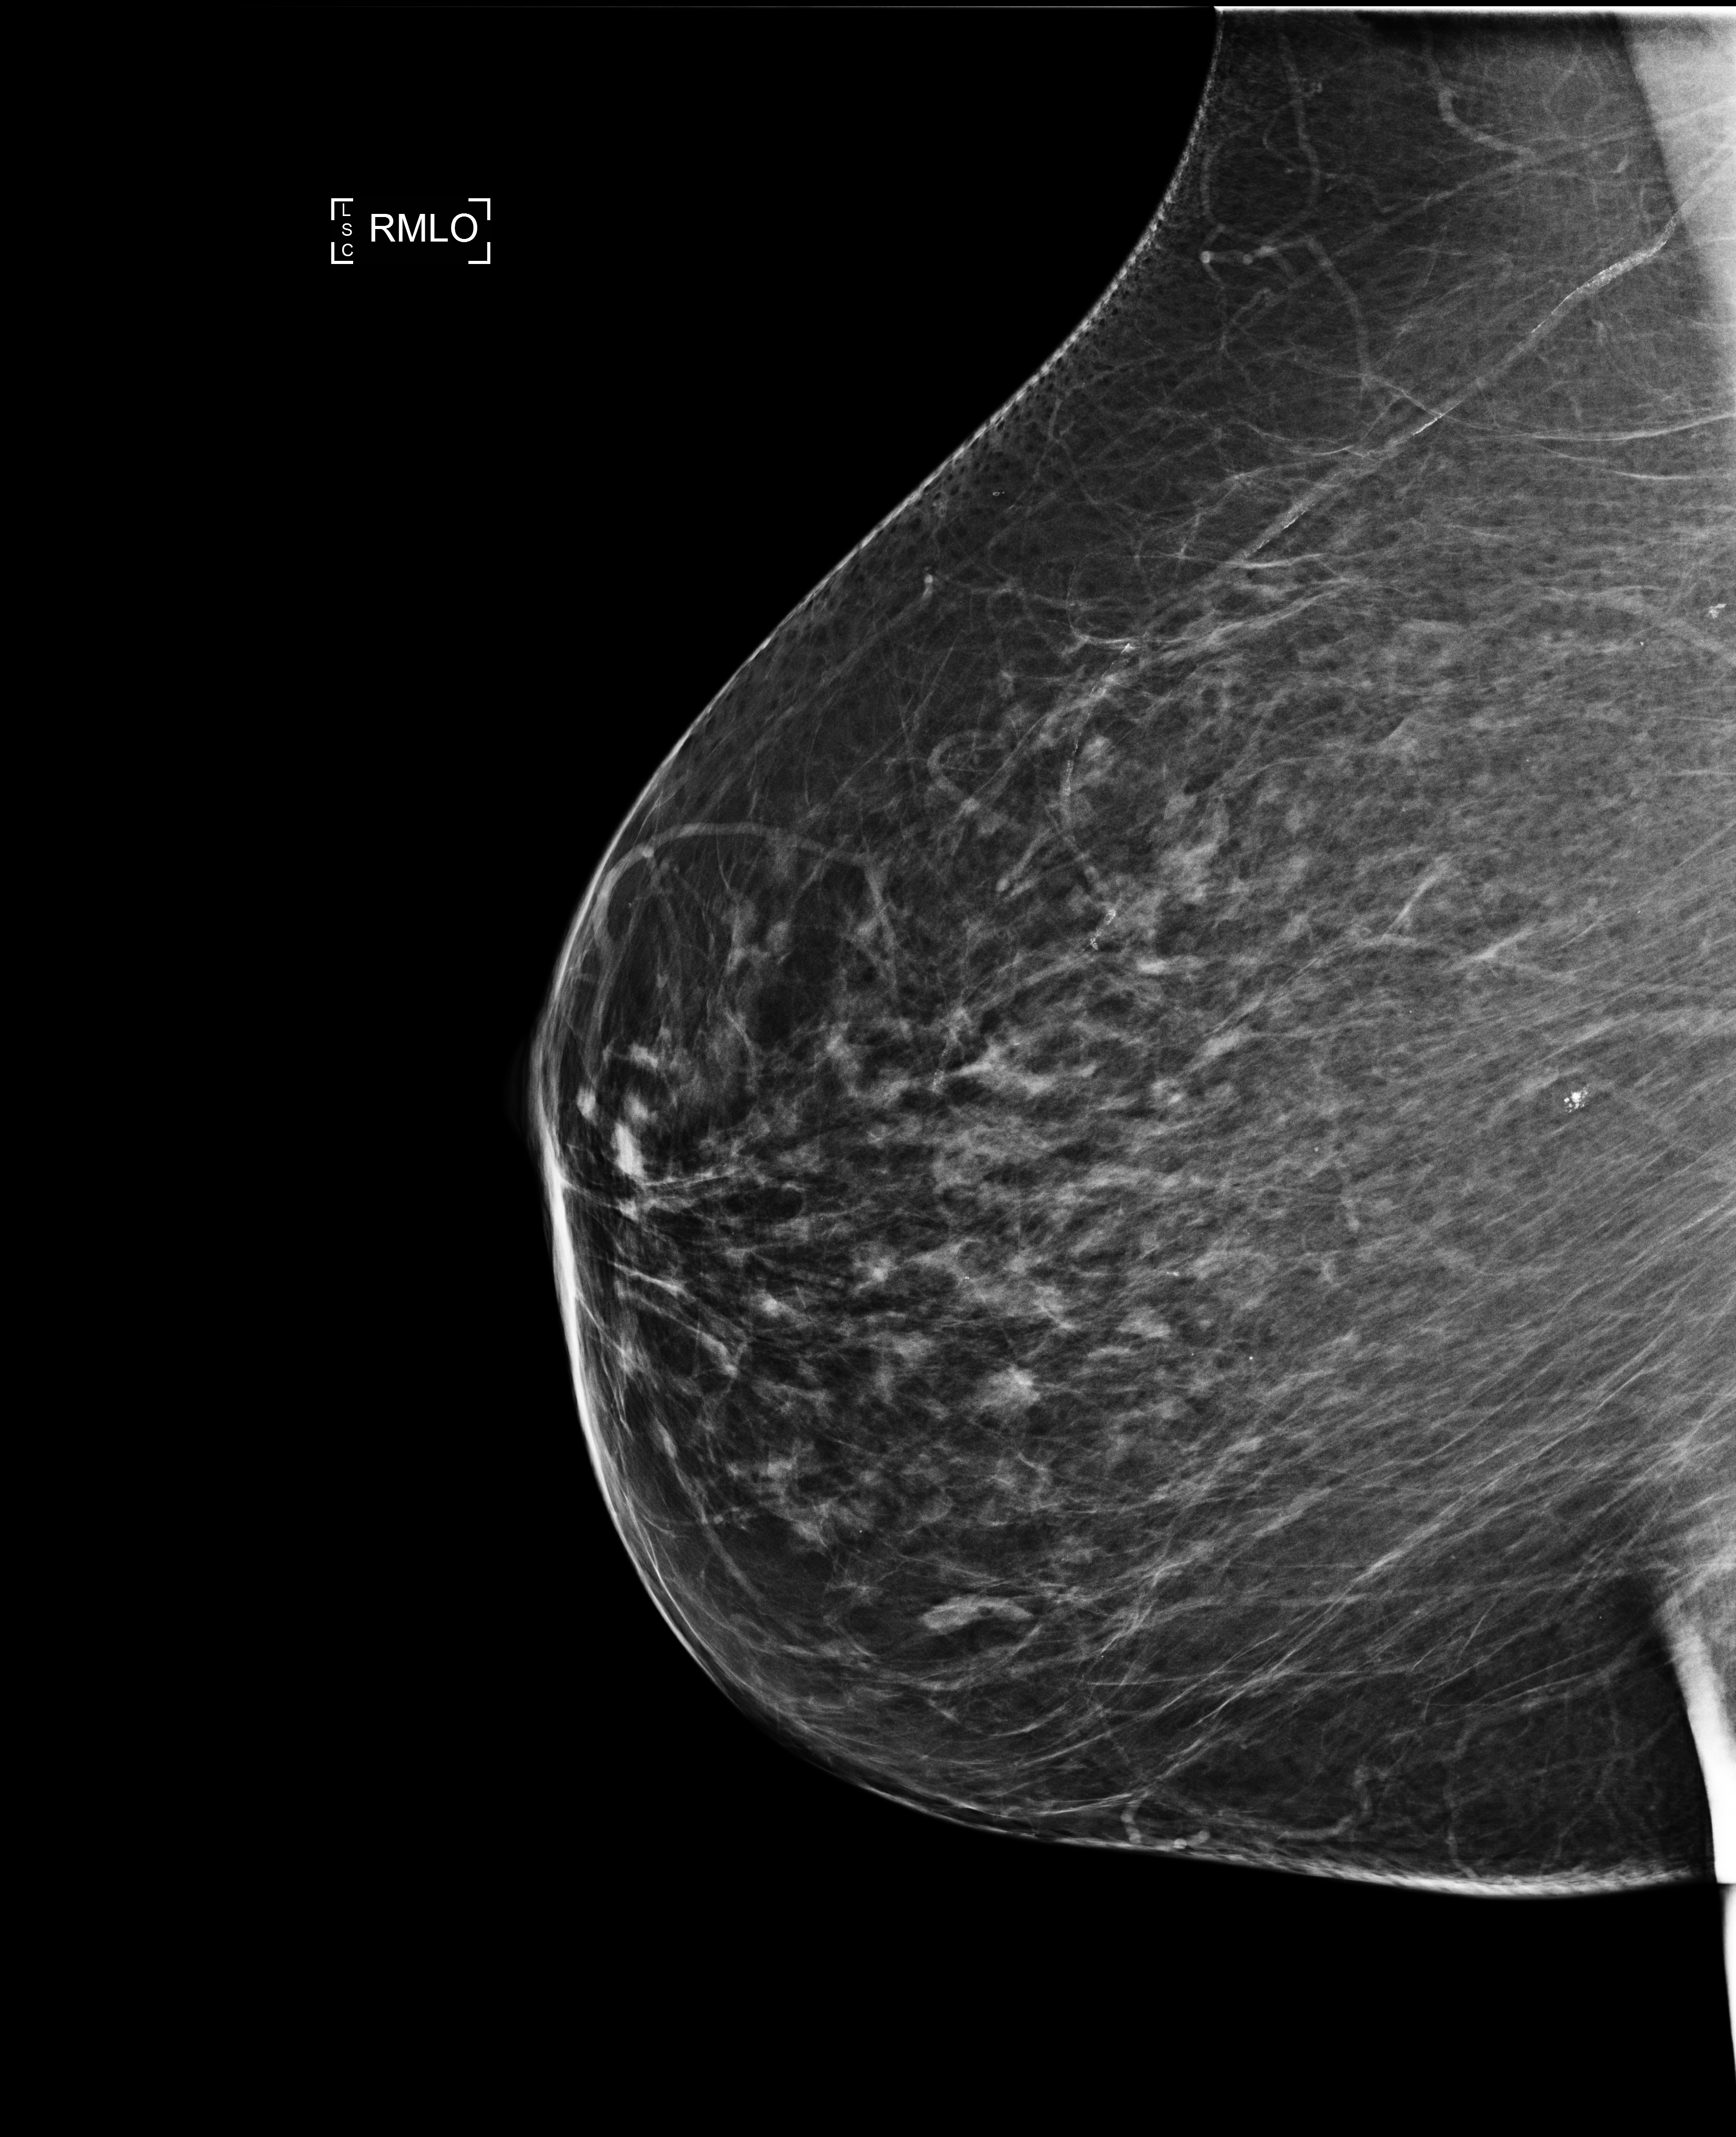
Digital mammogram (FFDM); right breast; medio-lateral oblique projection; screening examination. Patient: female, 73 years.
BI-RADS breast density category at the screening exam (both breasts, scale 1–4): 3. Final BI-RADS assessment for this screening round (tomosynthesis exam, both breasts): category 1. Recall: no recall after this screen.